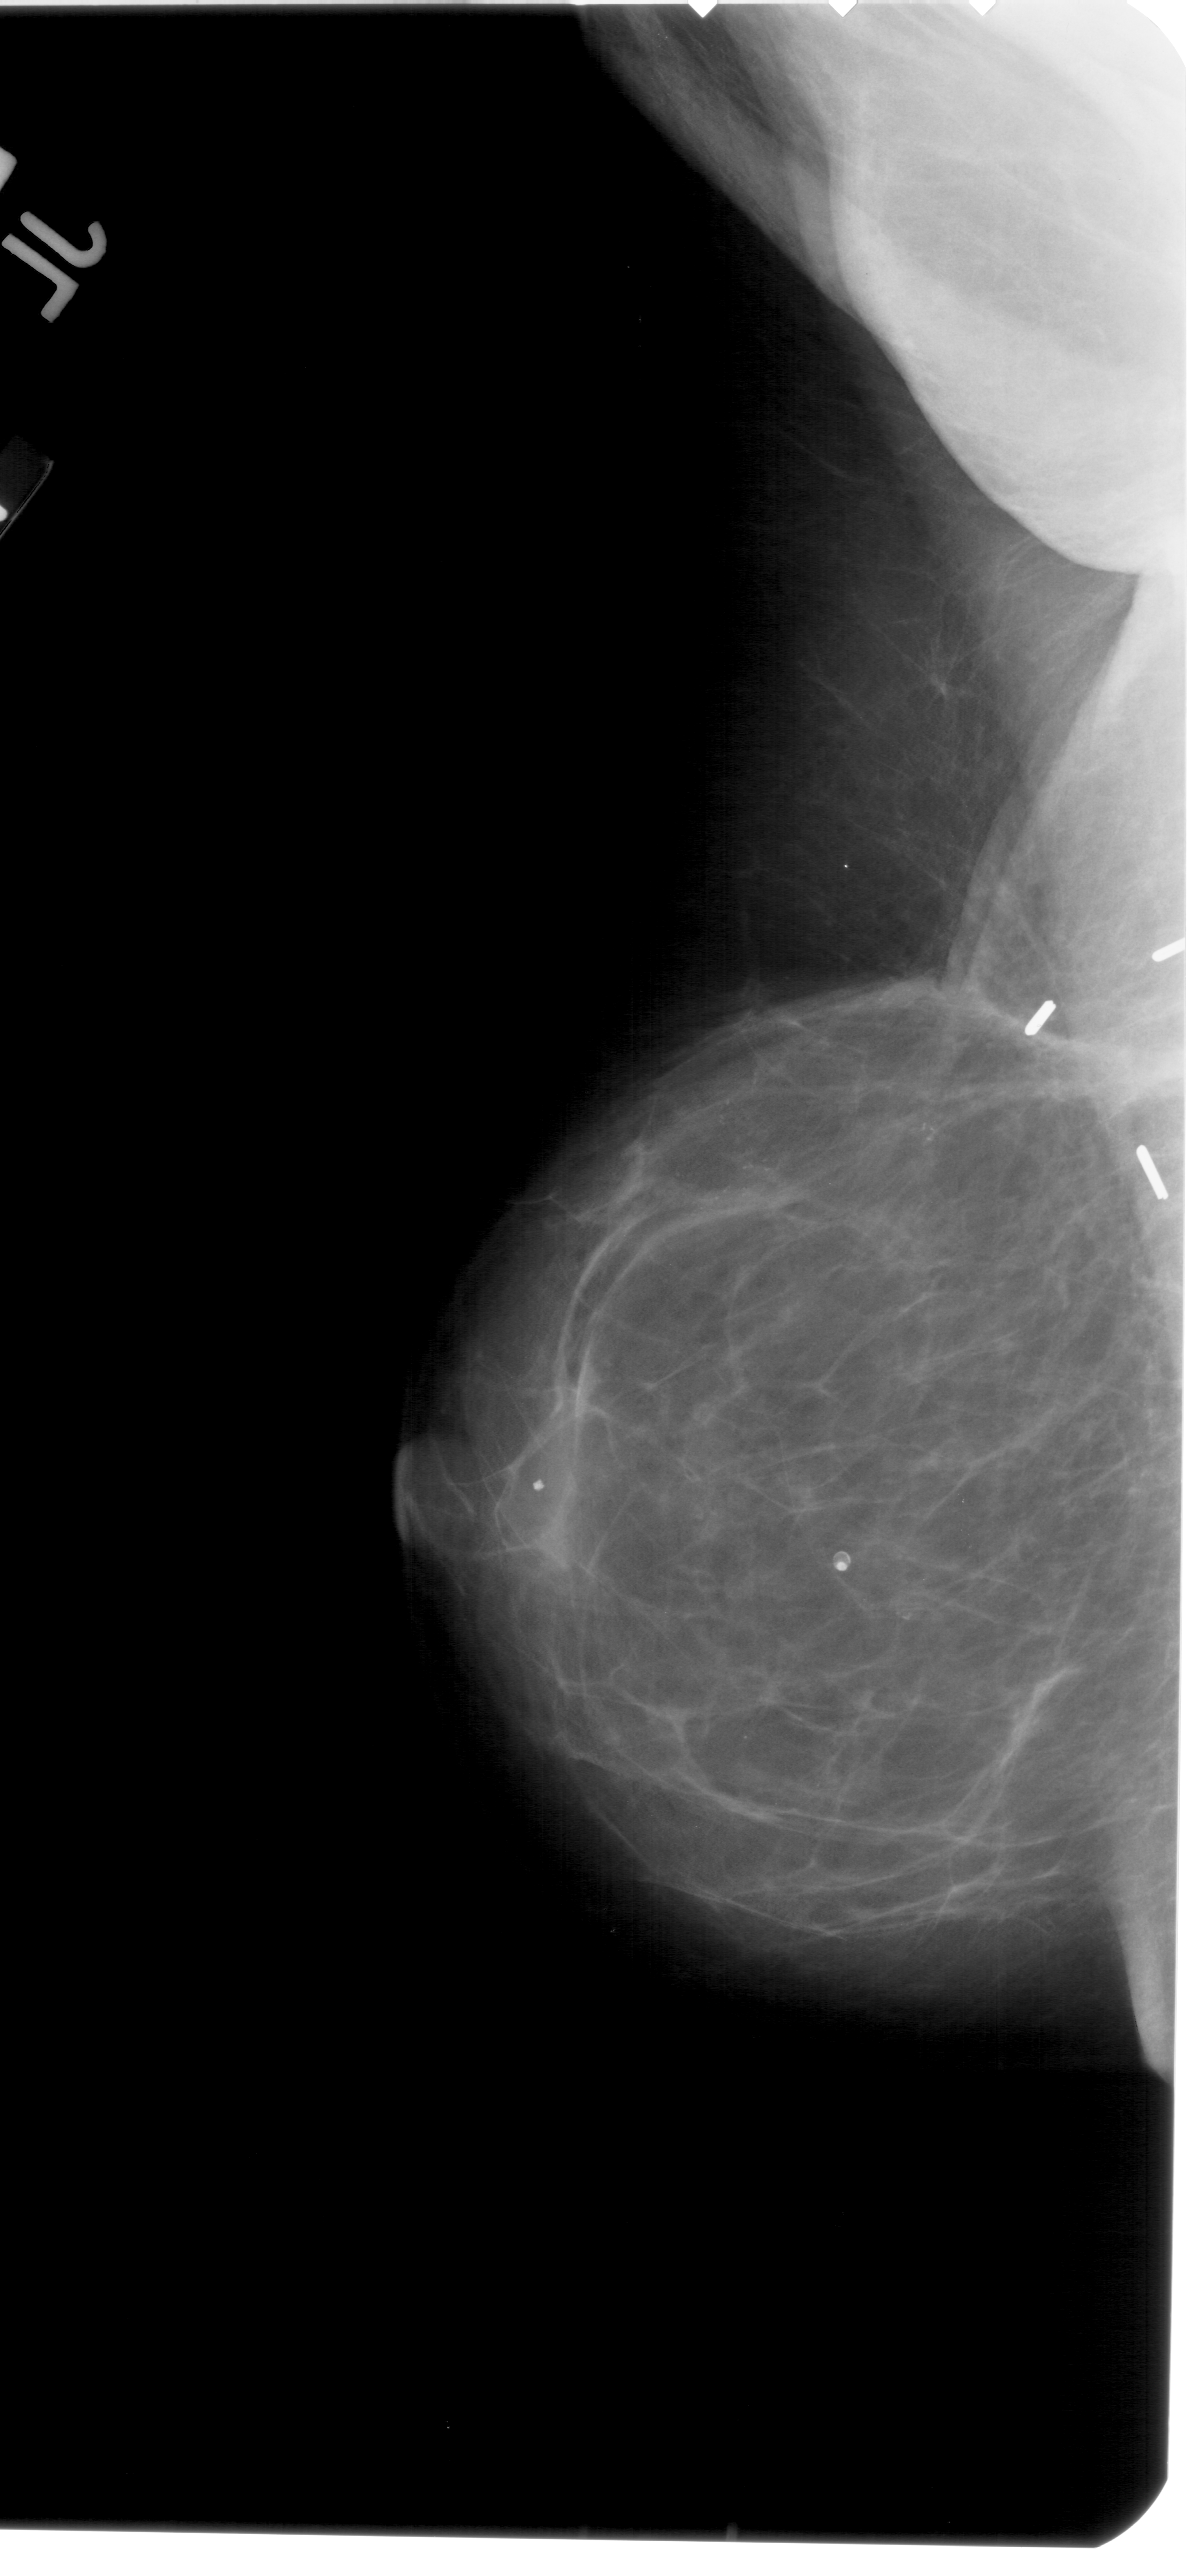
Scanned film-screen mammogram, left breast, MLO view, breast composition: heterogeneously dense (BI-RADS density category 3 of 4).
- Marked findings (only marked abnormalities are described; nothing is implied about the rest of the image): calcifications, morphology pleomorphic, distribution linear; BI-RADS assessment category 5; pathology result (as recorded, not read from the image): malignant.